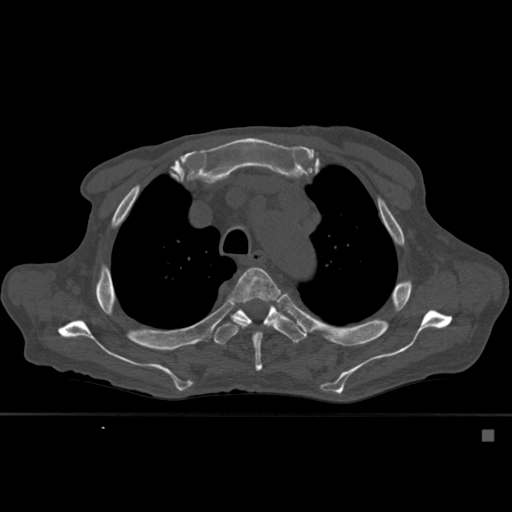
CT including the spine, one axial slice. Position 410 of 527 along the scan axis. Bone window (W 1800 / L 400 HU). 512 × 512 image matrix, field of view 373 × 373 mm. Patient: male, 78 years. From the clinical record (not read from this slice): primary cancer: prostate.
Structures marked on this image (semi-automatic segmentation, software-assisted and operator-edited):
- T4 vertebra: bounding box <229,267,281,371> (left, top, right, bottom; pixels)
- T5 vertebra: <213,299,307,346>